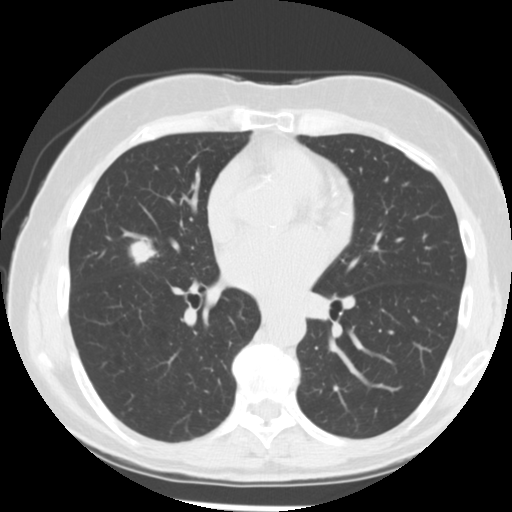
Low-dose screening chest CT, one axial slice; position 135 of 255 along the scan axis; reconstruction kernel STANDARD; 120 kVp; lung window (W 1500 / L -600 HU); 2.5 mm slice thickness; 512 × 512 image matrix.
Annotated regions visible in this slice (outlined manually by an expert reader):
- lesion 1 (tumor, middle lobe of right lung): box from (x=129, y=240) to (x=158, y=265) px